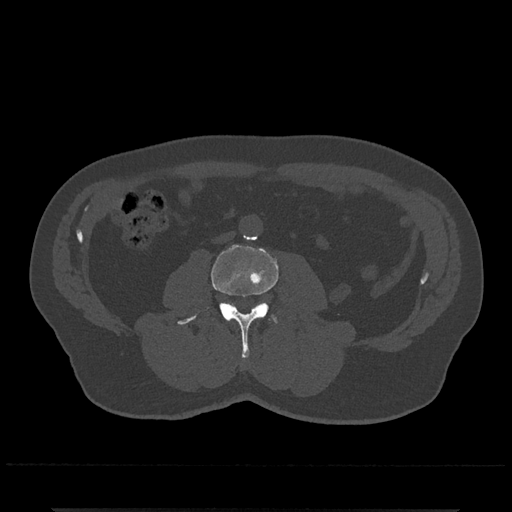
CT including the spine, one axial slice. Position 215 of 797 along the scan axis. Reconstruction kernel Br40s/3. Bone window (W 1800 / L 400 HU). 0.5 mm slice thickness. 512 × 512 image matrix, field of view 393 × 393 mm. Male patient, age 67 years. Case-level facts recorded for this patient, not image findings: primary cancer: prostate.
Outlined on this slice (semi-automatically segmented with operator editing):
- L3 vertebra: box from (x=177, y=245) to (x=279, y=358) px
- L4 vertebra: (x=274, y=318)–(x=277, y=322)